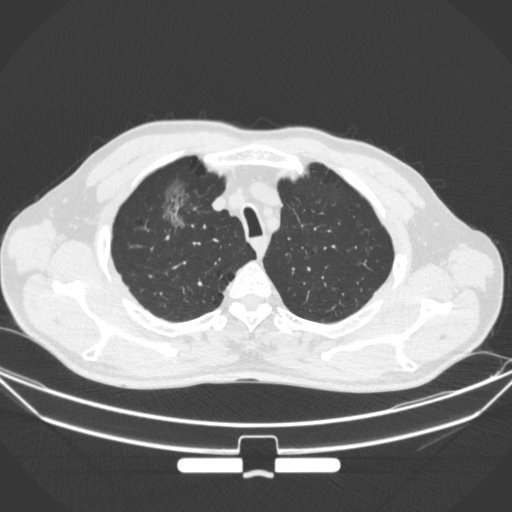
Chest CT, one axial slice. Slice 288 of 355 in the series (ordered by position). 120 kVp. Lung window (W 1500 / L -600 HU). 1 mm slice thickness. 512 × 512 image matrix, field of view 399 × 399 mm. Male patient, age 67 years. From the clinical record (not read from this slice): clinical TNM (as recorded): T1c N0 M0.
Structures marked on this image (rectangle marked by the reading radiologist):
- lung tumour (recorded histology: adenocarcinoma): bounding box <156,176,197,230> (left, top, right, bottom; pixels)